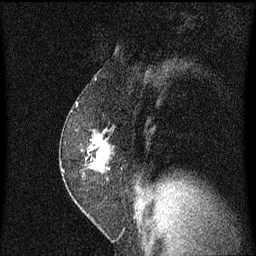
Breast MRI (dynamic contrast-enhanced), one sagittal slice; slice 39 of 60 in the series (ordered by position); dynamic contrast-enhanced series, image 2 of 3 at this slice position (ordered by acquisition); 1.5 T; TE 4.2 ms, TR 8.4 ms; 2 mm slice thickness; 256 × 256 image matrix, field of view 200 × 200 mm. Patient: female, 52 years. Case-level facts recorded for this patient, not image findings: setting: breast cancer imaged before/during neoadjuvant chemotherapy; receptor status: HER2-positive.
Annotated regions visible in this slice (semi-automatic segmentation, software-assisted and operator-edited):
- analysis volume of interest (the breast-tissue region the enhancement analysis was run in; not a lesion): box from (x=61, y=124) to (x=116, y=191) px
- tumour enhancement mask (voxels above the 70 % enhancement threshold inside the analysis volume of interest): (x=91, y=130)–(x=108, y=169)